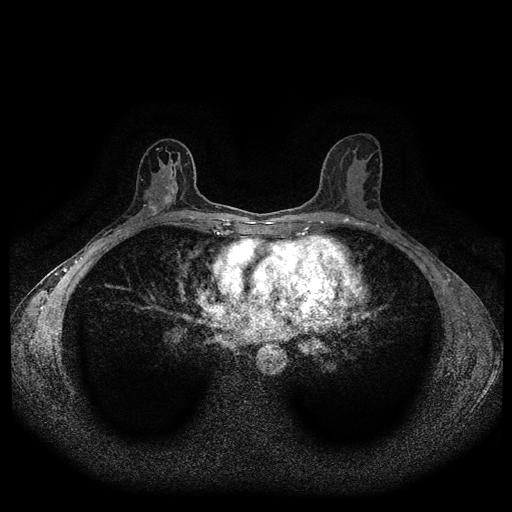
Breast MRI (dynamic contrast-enhanced, multi-phase), one axial slice. Position 56 of 116 along the scan axis. Dynamic contrast-enhanced series, time point 2 of 5 at this slice position (early post-contrast). 1.5 T. TE 2.6 ms, TR 5.3 ms. 2 mm slice thickness. 512 × 512 image matrix, field of view 350 × 350 mm. Female patient, age 50 years.
Outlined on this slice (semi-automatic segmentation, software-assisted and operator-edited):
- breast lesion (labelled 'tumour' in the annotation; benign lesions carry a separate 'benign' label): bounding box [x1, y1, x2, y2] px = [146, 193, 176, 216]